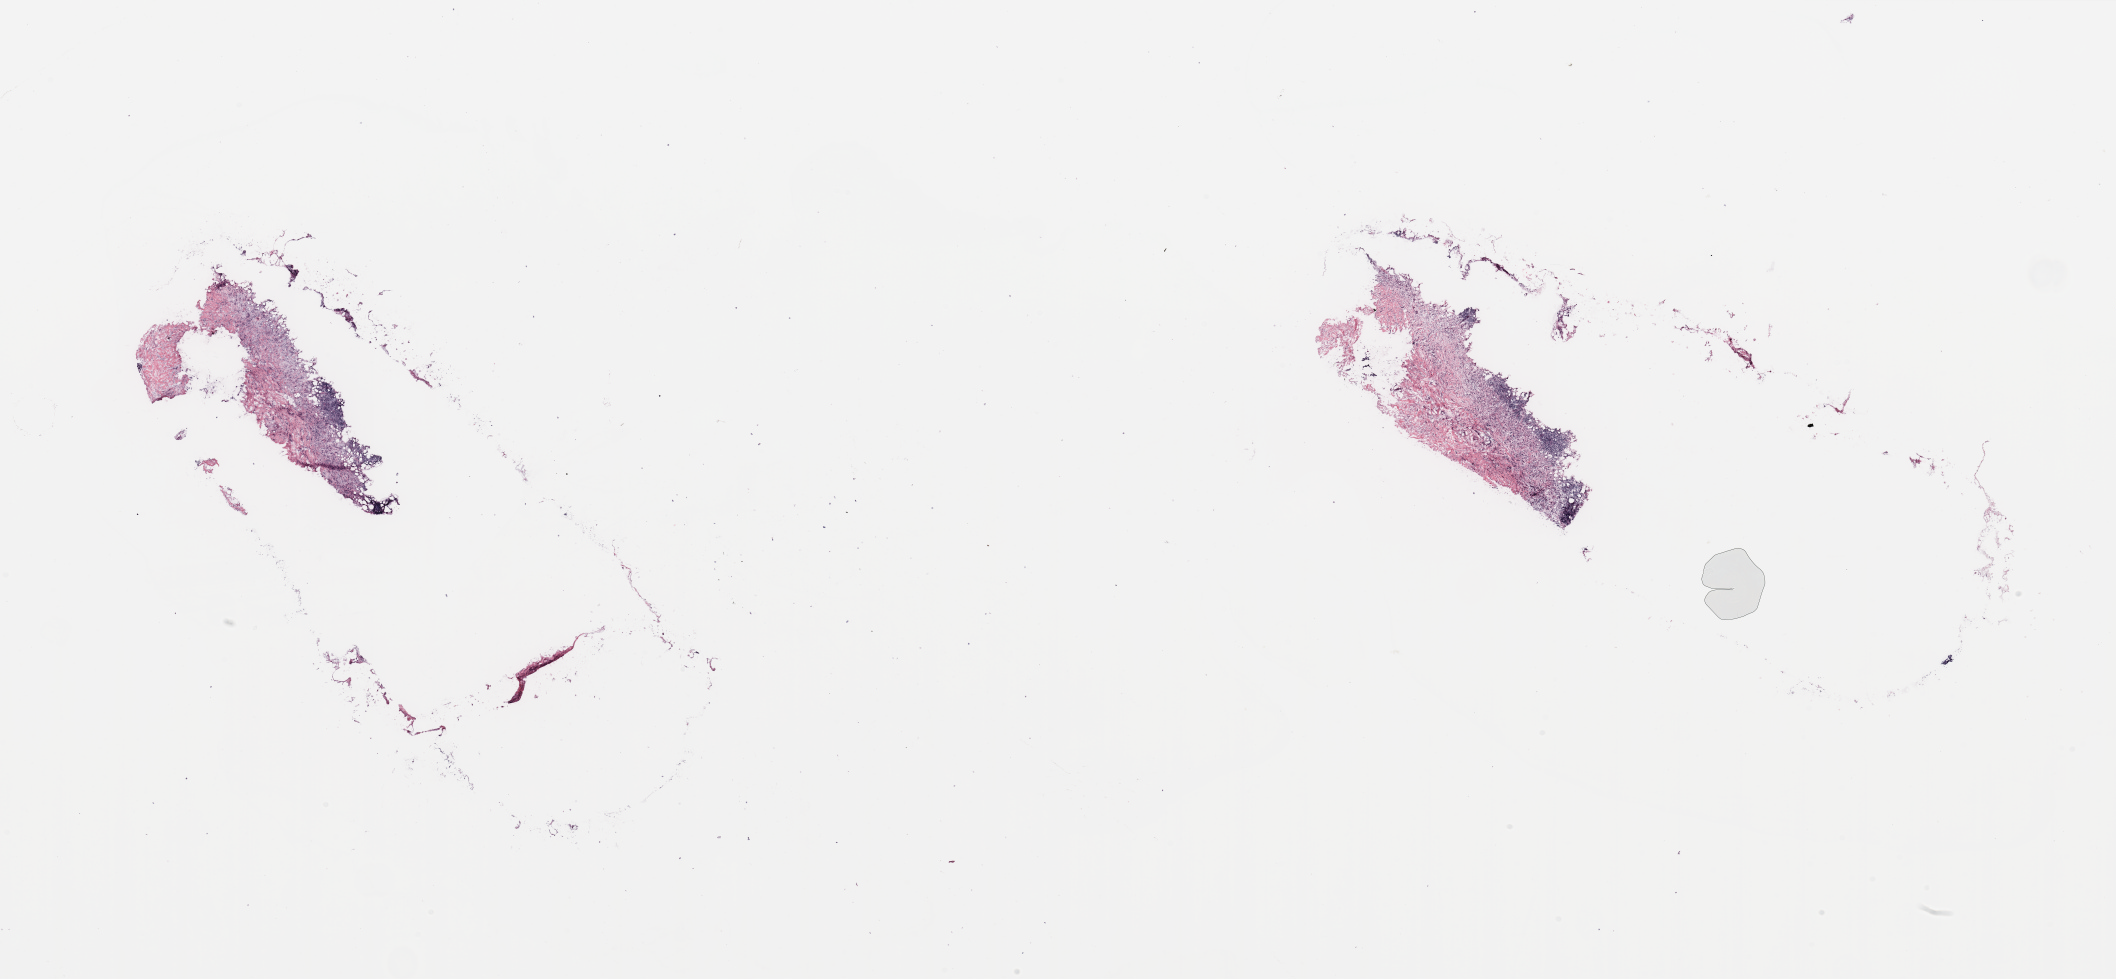
Digitized H&E-stained tissue section (whole slide) — whole scanned area (about 33.5 x 15.5 mm, from a 20x scan) shown as a low-resolution overview. Breast, tissue type not recorded.
* patient diagnosis (cohort enrolment): breast cancer (breast)